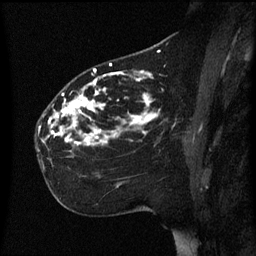
Breast MRI (dynamic contrast-enhanced), one sagittal slice; slice 35 of 60 in the series (ordered by position); dynamic contrast-enhanced series, image 2 of 3 at this slice position (ordered by acquisition); 1.5 T; TE 4.2 ms, TR 8.4 ms; 256 × 256 image matrix, field of view 200 × 200 mm. Patient: female, 35 years. Case-level facts recorded for this patient, not image findings: setting: breast cancer imaged before/during neoadjuvant chemotherapy; receptor status: HER2-positive.
Outlined on this slice (semi-automatic segmentation, software-assisted and operator-edited):
- analysis volume of interest (the breast-tissue region the enhancement analysis was run in; not a lesion): box from (x=37, y=78) to (x=169, y=163) px
- tumour enhancement mask (voxels above the 70 % enhancement threshold inside the analysis volume of interest): (x=40, y=78)–(x=159, y=147)